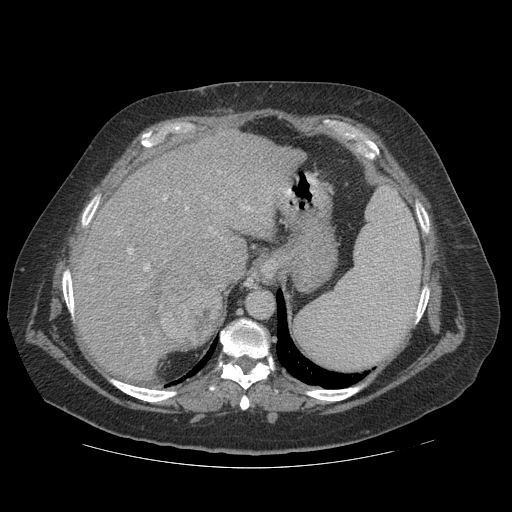
Contrast-enhanced abdominal CT (liver protocol), one axial slice; slice 88 of 121 in the series (ordered by position); reconstruction kernel STANDARD; 140 kVp; soft-tissue window (W 400 / L 40 HU); 512 × 512 image matrix, field of view 420 × 420 mm. Case-level facts recorded for this patient, not image findings: diagnosis: hepatocellular carcinoma (patient treated with transarterial chemoembolisation; whether this scan precedes or follows treatment is not stated here); TNM stage (as recorded): Stage-IIIA; Child-Pugh class: A; tumour differentiation: well differentiated; tumour nodularity: multinodular.
Outlined on this slice (semi-automatic segmentation, software-assisted and operator-edited):
- liver parenchyma outside the tumour (the mass and vessels are separate outlines, so this box may not span the whole liver): box from (x=72, y=128) to (x=306, y=380) px
- mass: (x=136, y=263)–(x=222, y=352)
- liver vessels: (x=115, y=167)–(x=285, y=353)